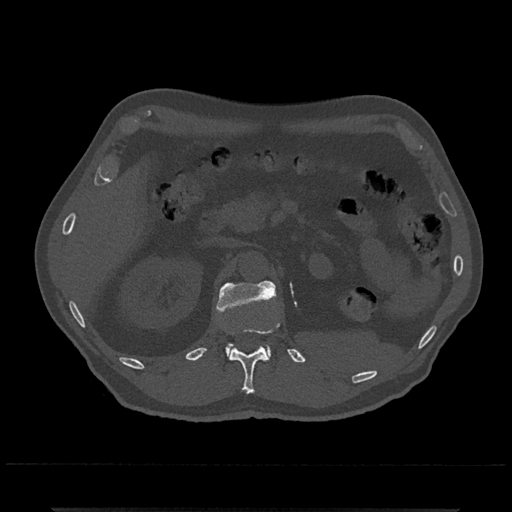
CT including the spine, one axial slice. Position 403 of 797 along the scan axis. Reconstruction kernel Br40s/3. 120 kVp. Bone window (W 1800 / L 400 HU). 0.5 mm slice thickness. 512 × 512 image matrix. Patient: male, 67 years. Case-level facts recorded for this patient, not image findings: primary cancer: prostate.
Annotated regions visible in this slice (semi-automatic segmentation, software-assisted and operator-edited):
- L1 vertebra: bounding box (x1, y1, x2, y2) in pixels: (216, 281, 277, 361)
- T12 vertebra: (230, 324, 279, 394)